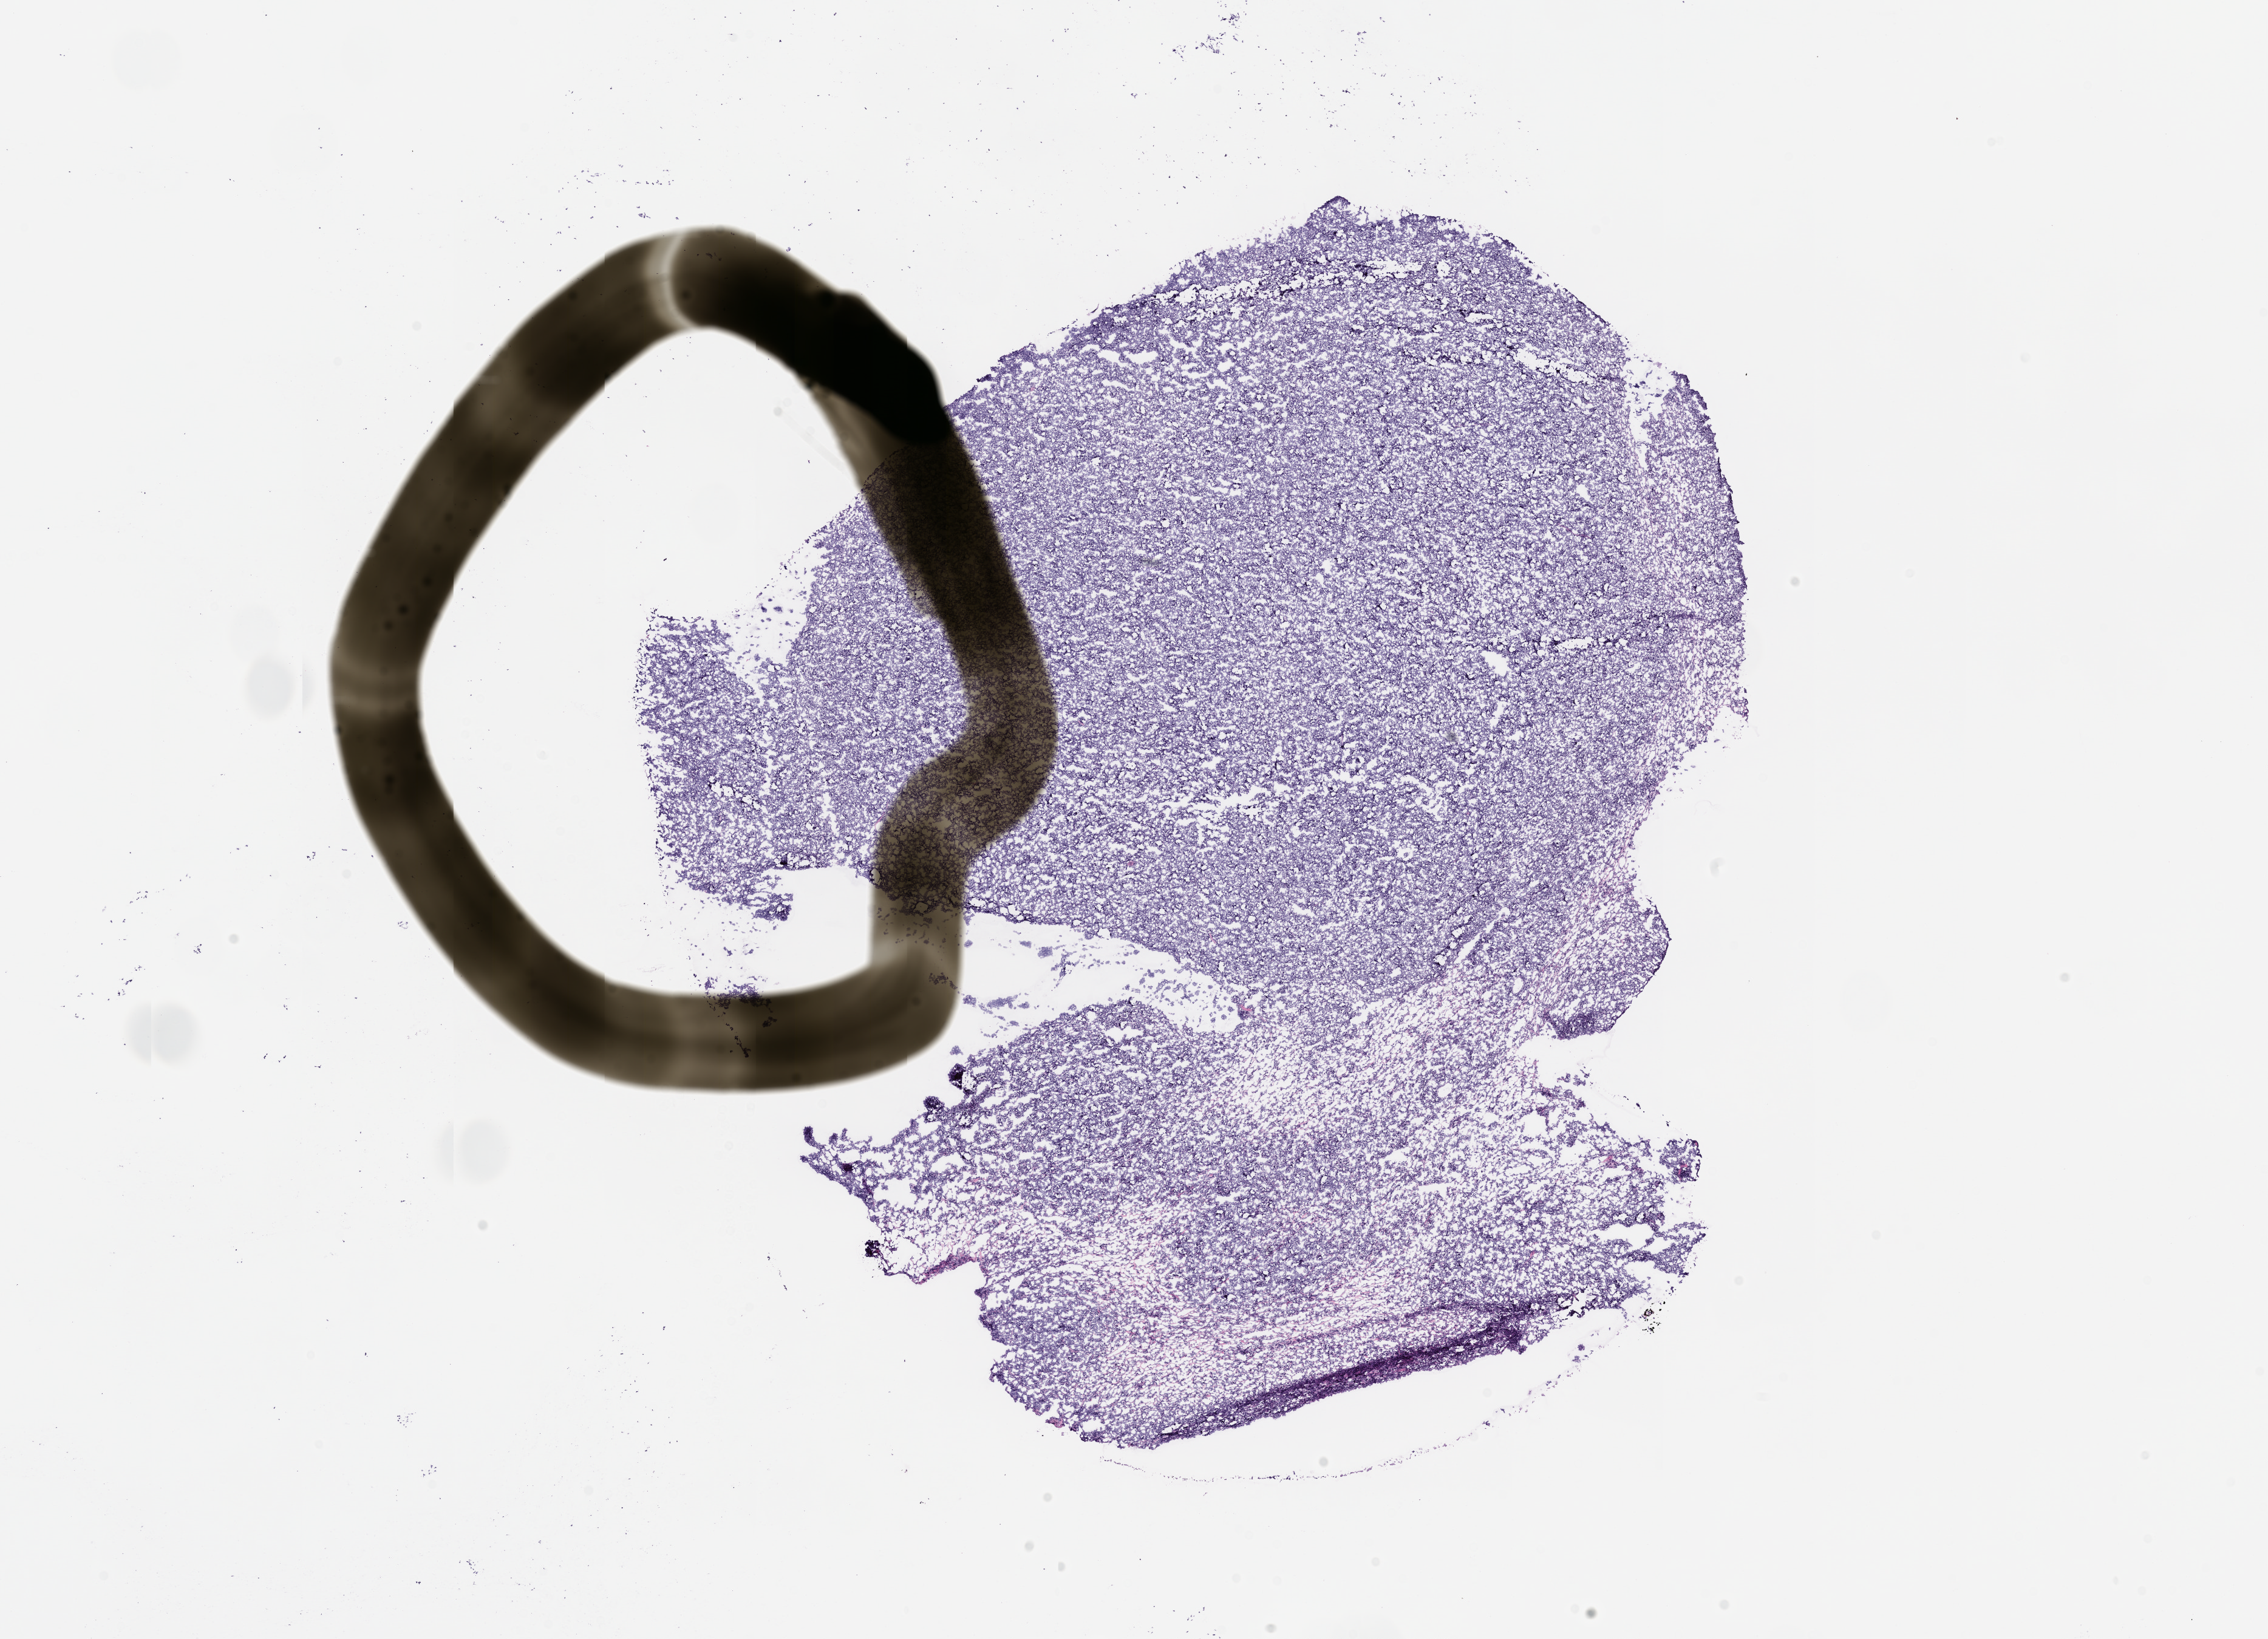
Whole-slide image, H&E: patient-derived xenograft (human tumor grown in a mouse), passage 0, whole scanned area (about 15.0 x 10.9 mm) shown as a low-resolution overview, FFPE section, tumor site category: musculoskeletal.
• originating patient diagnosis: Synovial Sarcoma